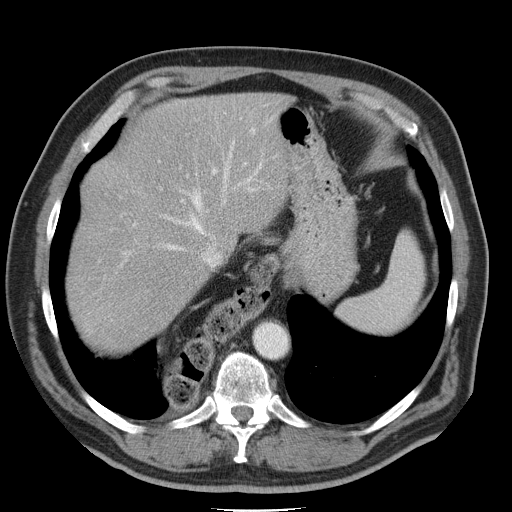
Contrast-enhanced abdominal CT, one axial slice. Position 37 of 45 along the scan axis. Intravenous contrast given. Soft-tissue window (W 400 / L 40 HU). 5 mm slice thickness. 512 × 512 image matrix, field of view 386 × 386 mm. Male patient, age 65 years. Case-level facts recorded for this patient, not image findings: diagnosis: colorectal cancer liver metastases, imaged before liver resection; multiple liver metastases: yes; largest metastasis: 4.9 cm; chemotherapy before resection: yes.
Outlined on this slice (manually delineated by an expert):
- hepatic veins: box from (x=85, y=118) to (x=263, y=335) px
- liver: (x=69, y=92)–(x=281, y=346)
- planned liver remnant (the part of the liver to remain after resection): (x=111, y=92)–(x=281, y=249)
- portal vein (with intrahepatic branches): (x=132, y=171)–(x=217, y=228)